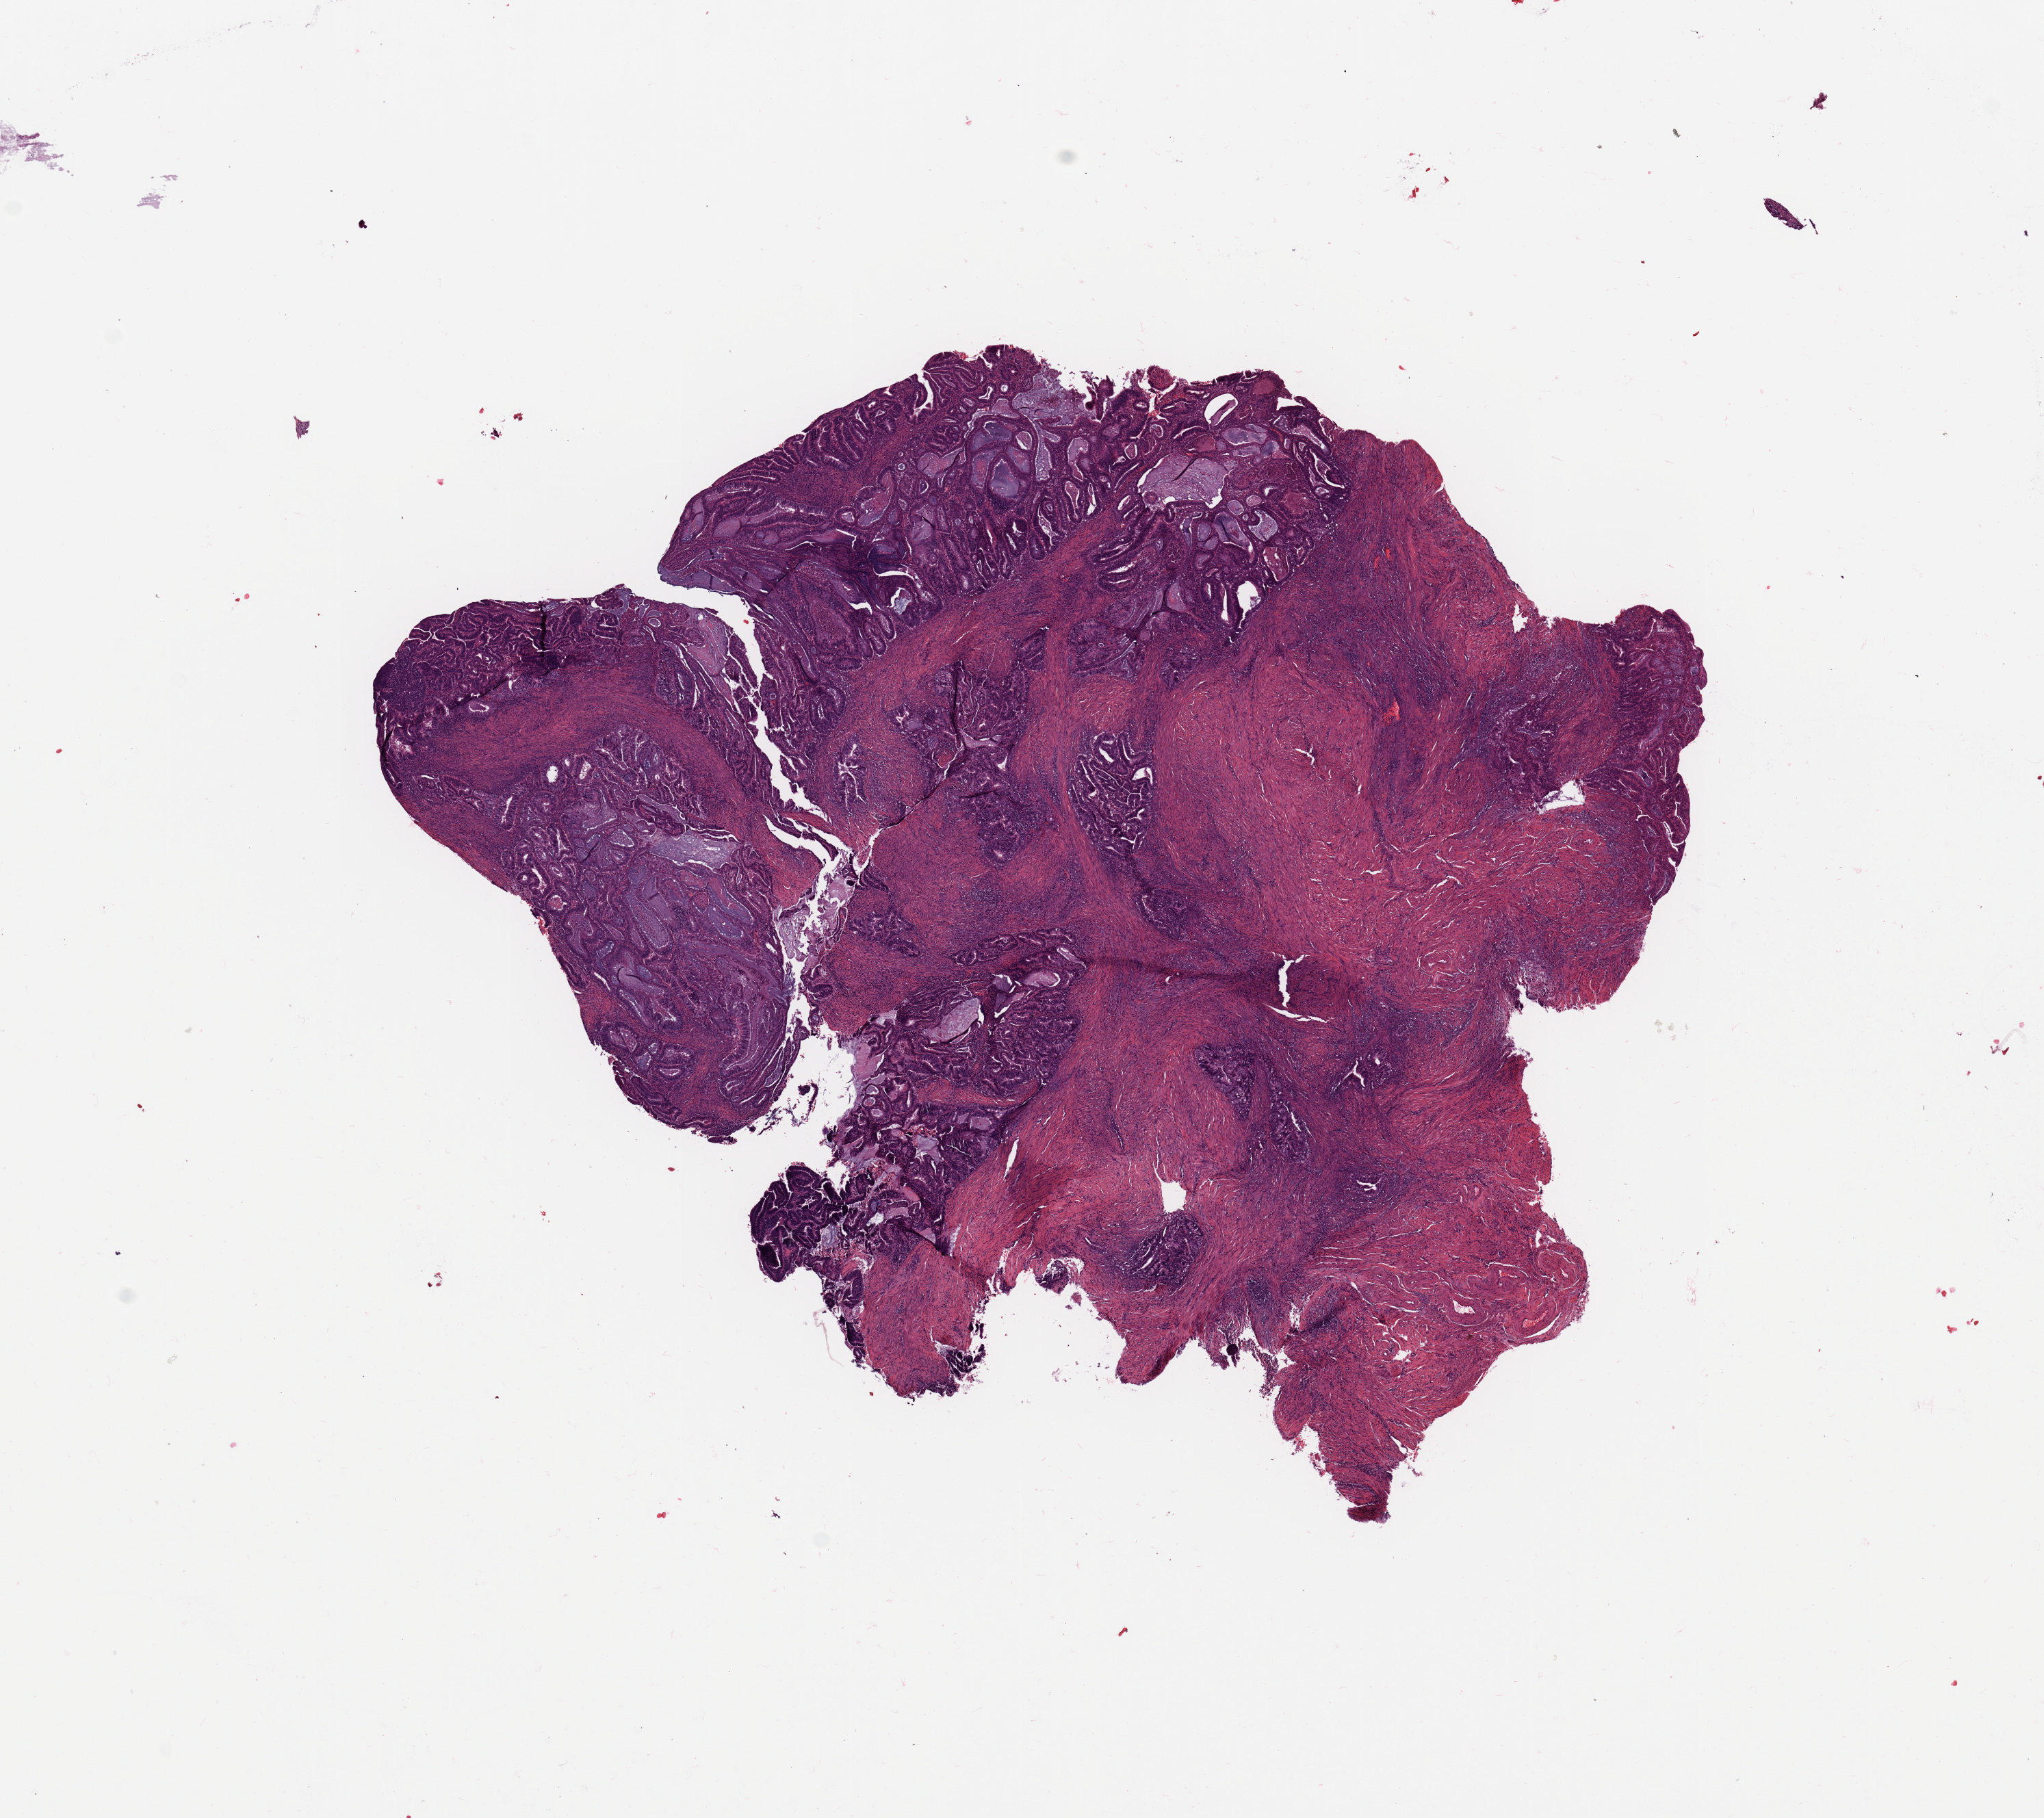
H&E-stained whole-slide image, low-resolution overview of the scanned area, about 11.8 x 10.5 mm, tumour tissue sample, sampled site: uterus. Female, 65 y/o. Histologic grade: G1 (well differentiated). Pathologist review of this section (percent, as recorded): tumour nuclei 80%, necrosis 0%.
AJCC pathologic stage: I. Histologic diagnosis: Endometrioid adenocarcinoma, NOS.